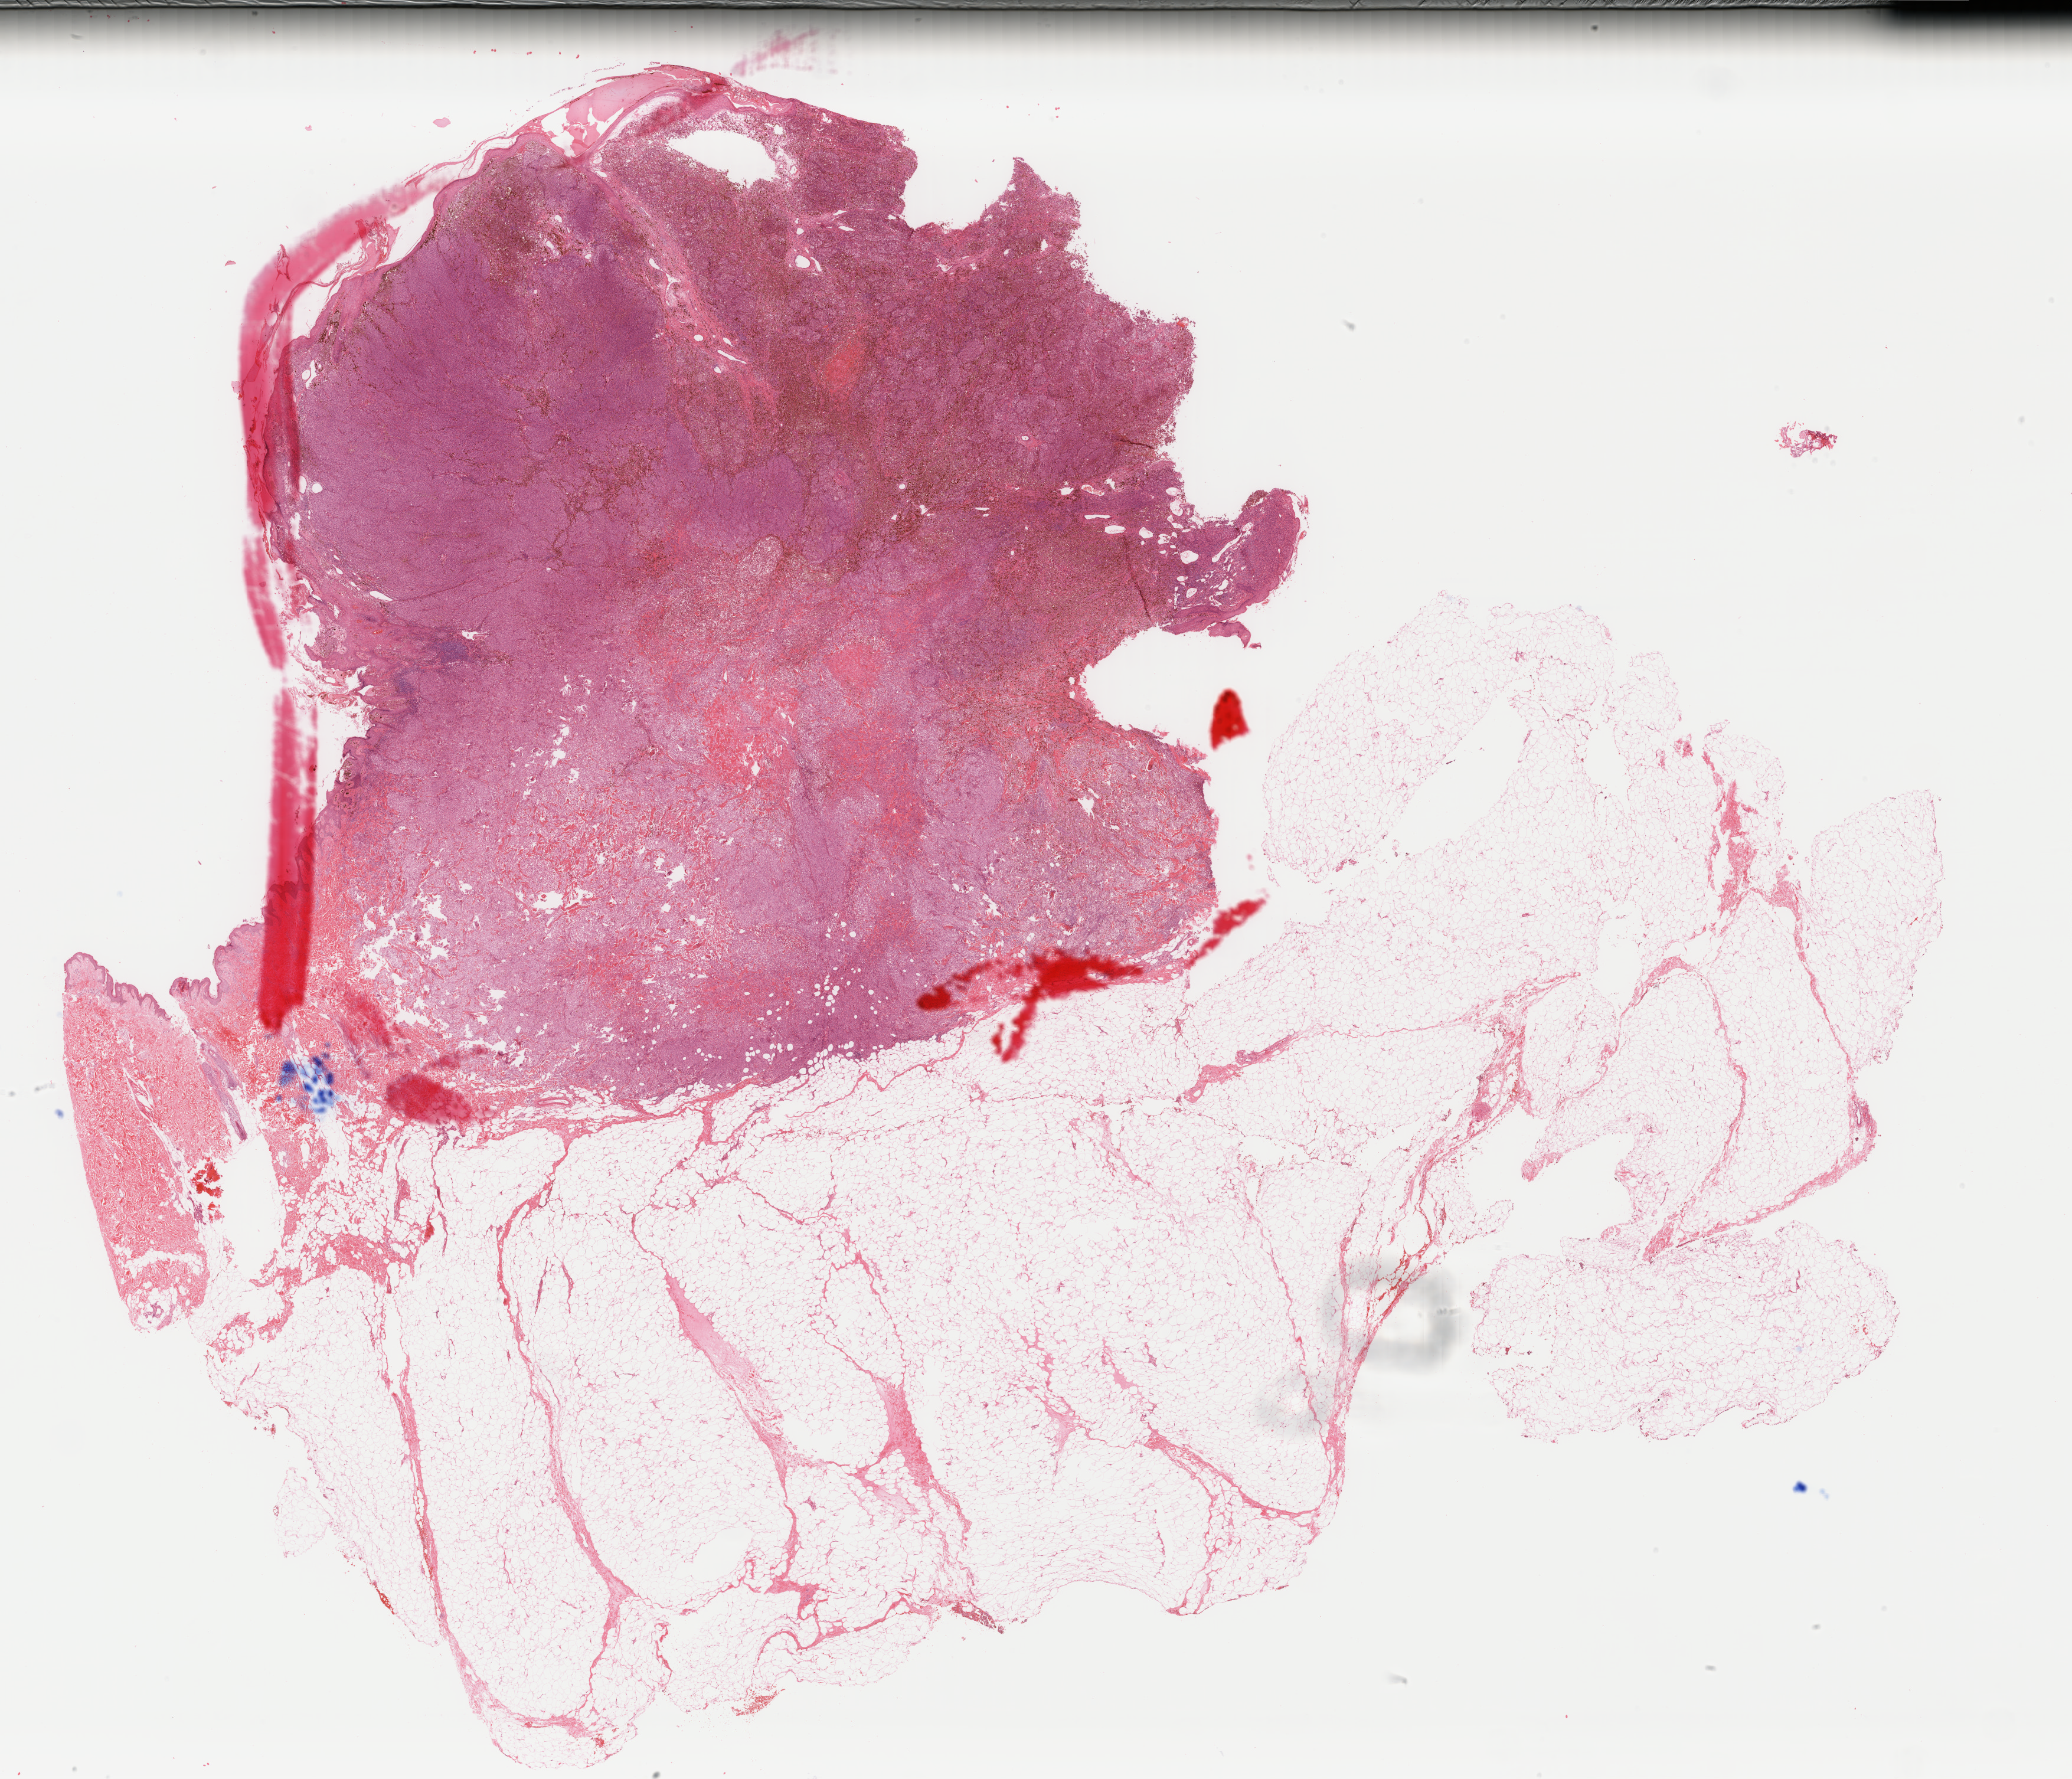
Whole-slide histology image, H&E — a low-resolution overview of the entire scanned area, about 27.9 x 23.9 mm (slide scanned at 40x), formalin-fixed paraffin-embedded (FFPE) diagnostic section, primary tumour sample from the skin. Female patient; age at initial diagnosis 41 years.
TNM: T4a N3 M0. AJCC pathologic stage: IIIC (7th edition). Histologic diagnosis: Malignant melanoma, NOS.